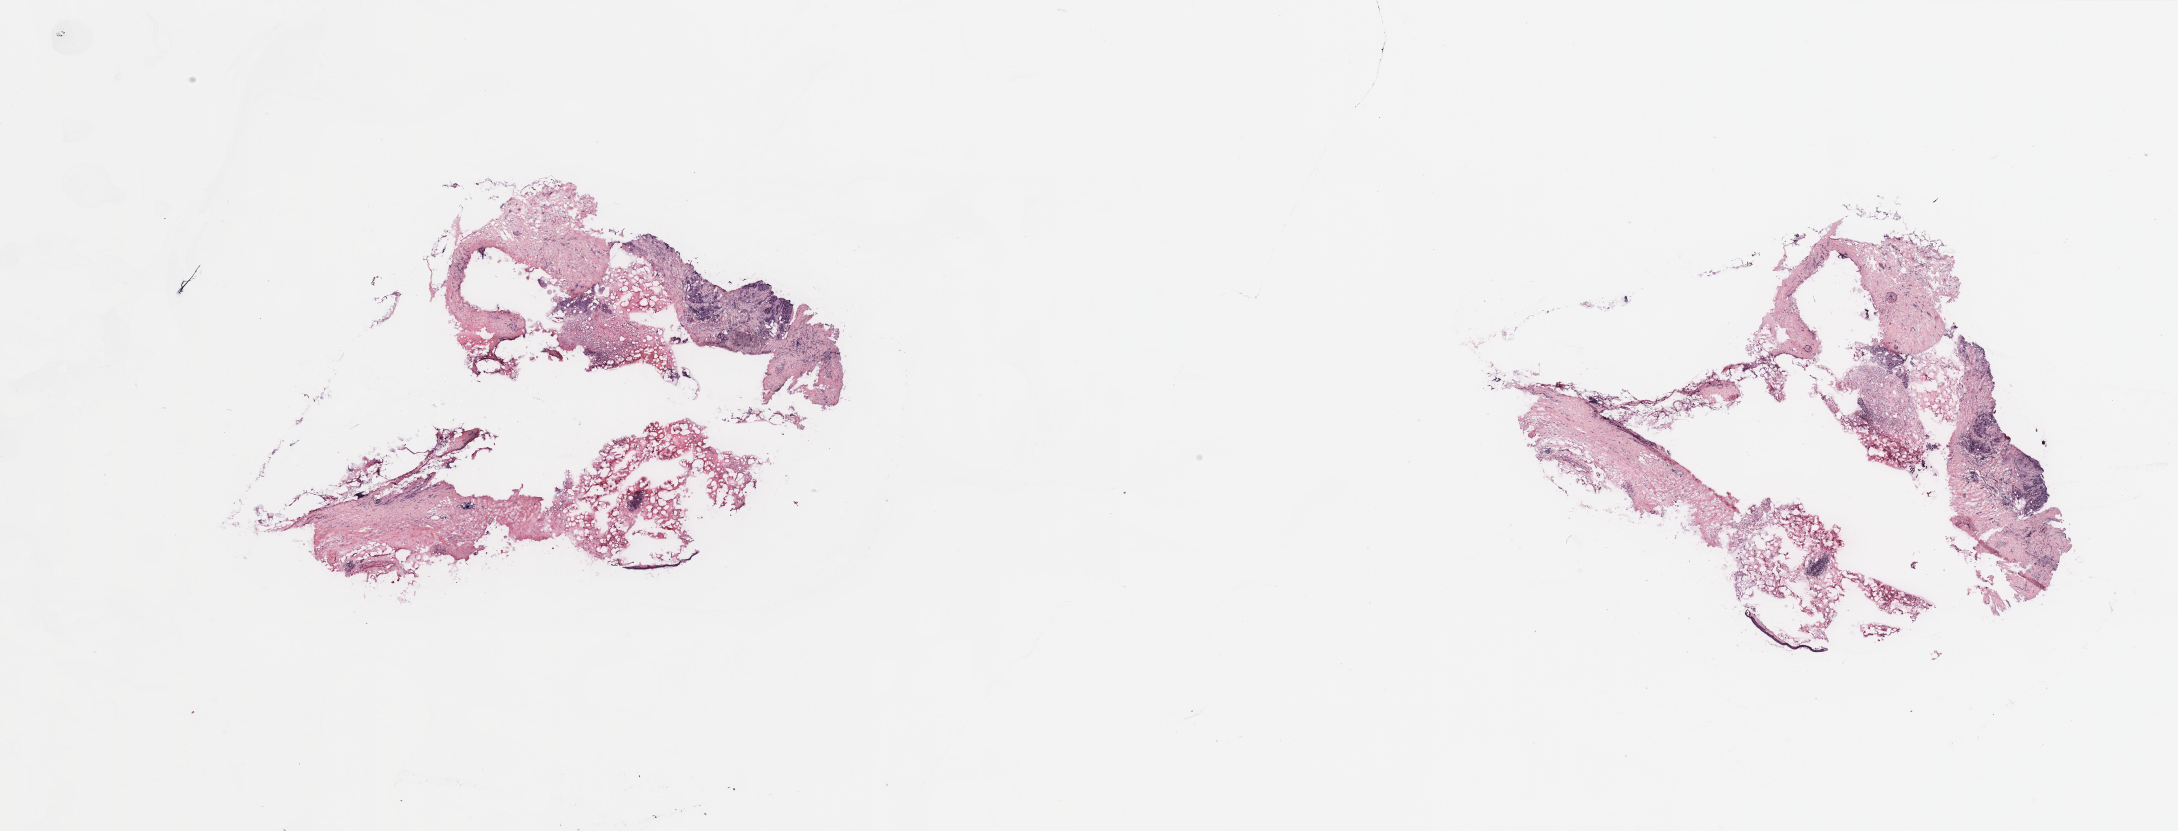
H&E-stained whole-slide image — shown as a low-resolution overview of the whole scanned area (about 34.5 x 13.1 mm); breast, tissue type not recorded.
• patient diagnosis (cohort enrolment): breast cancer (breast)